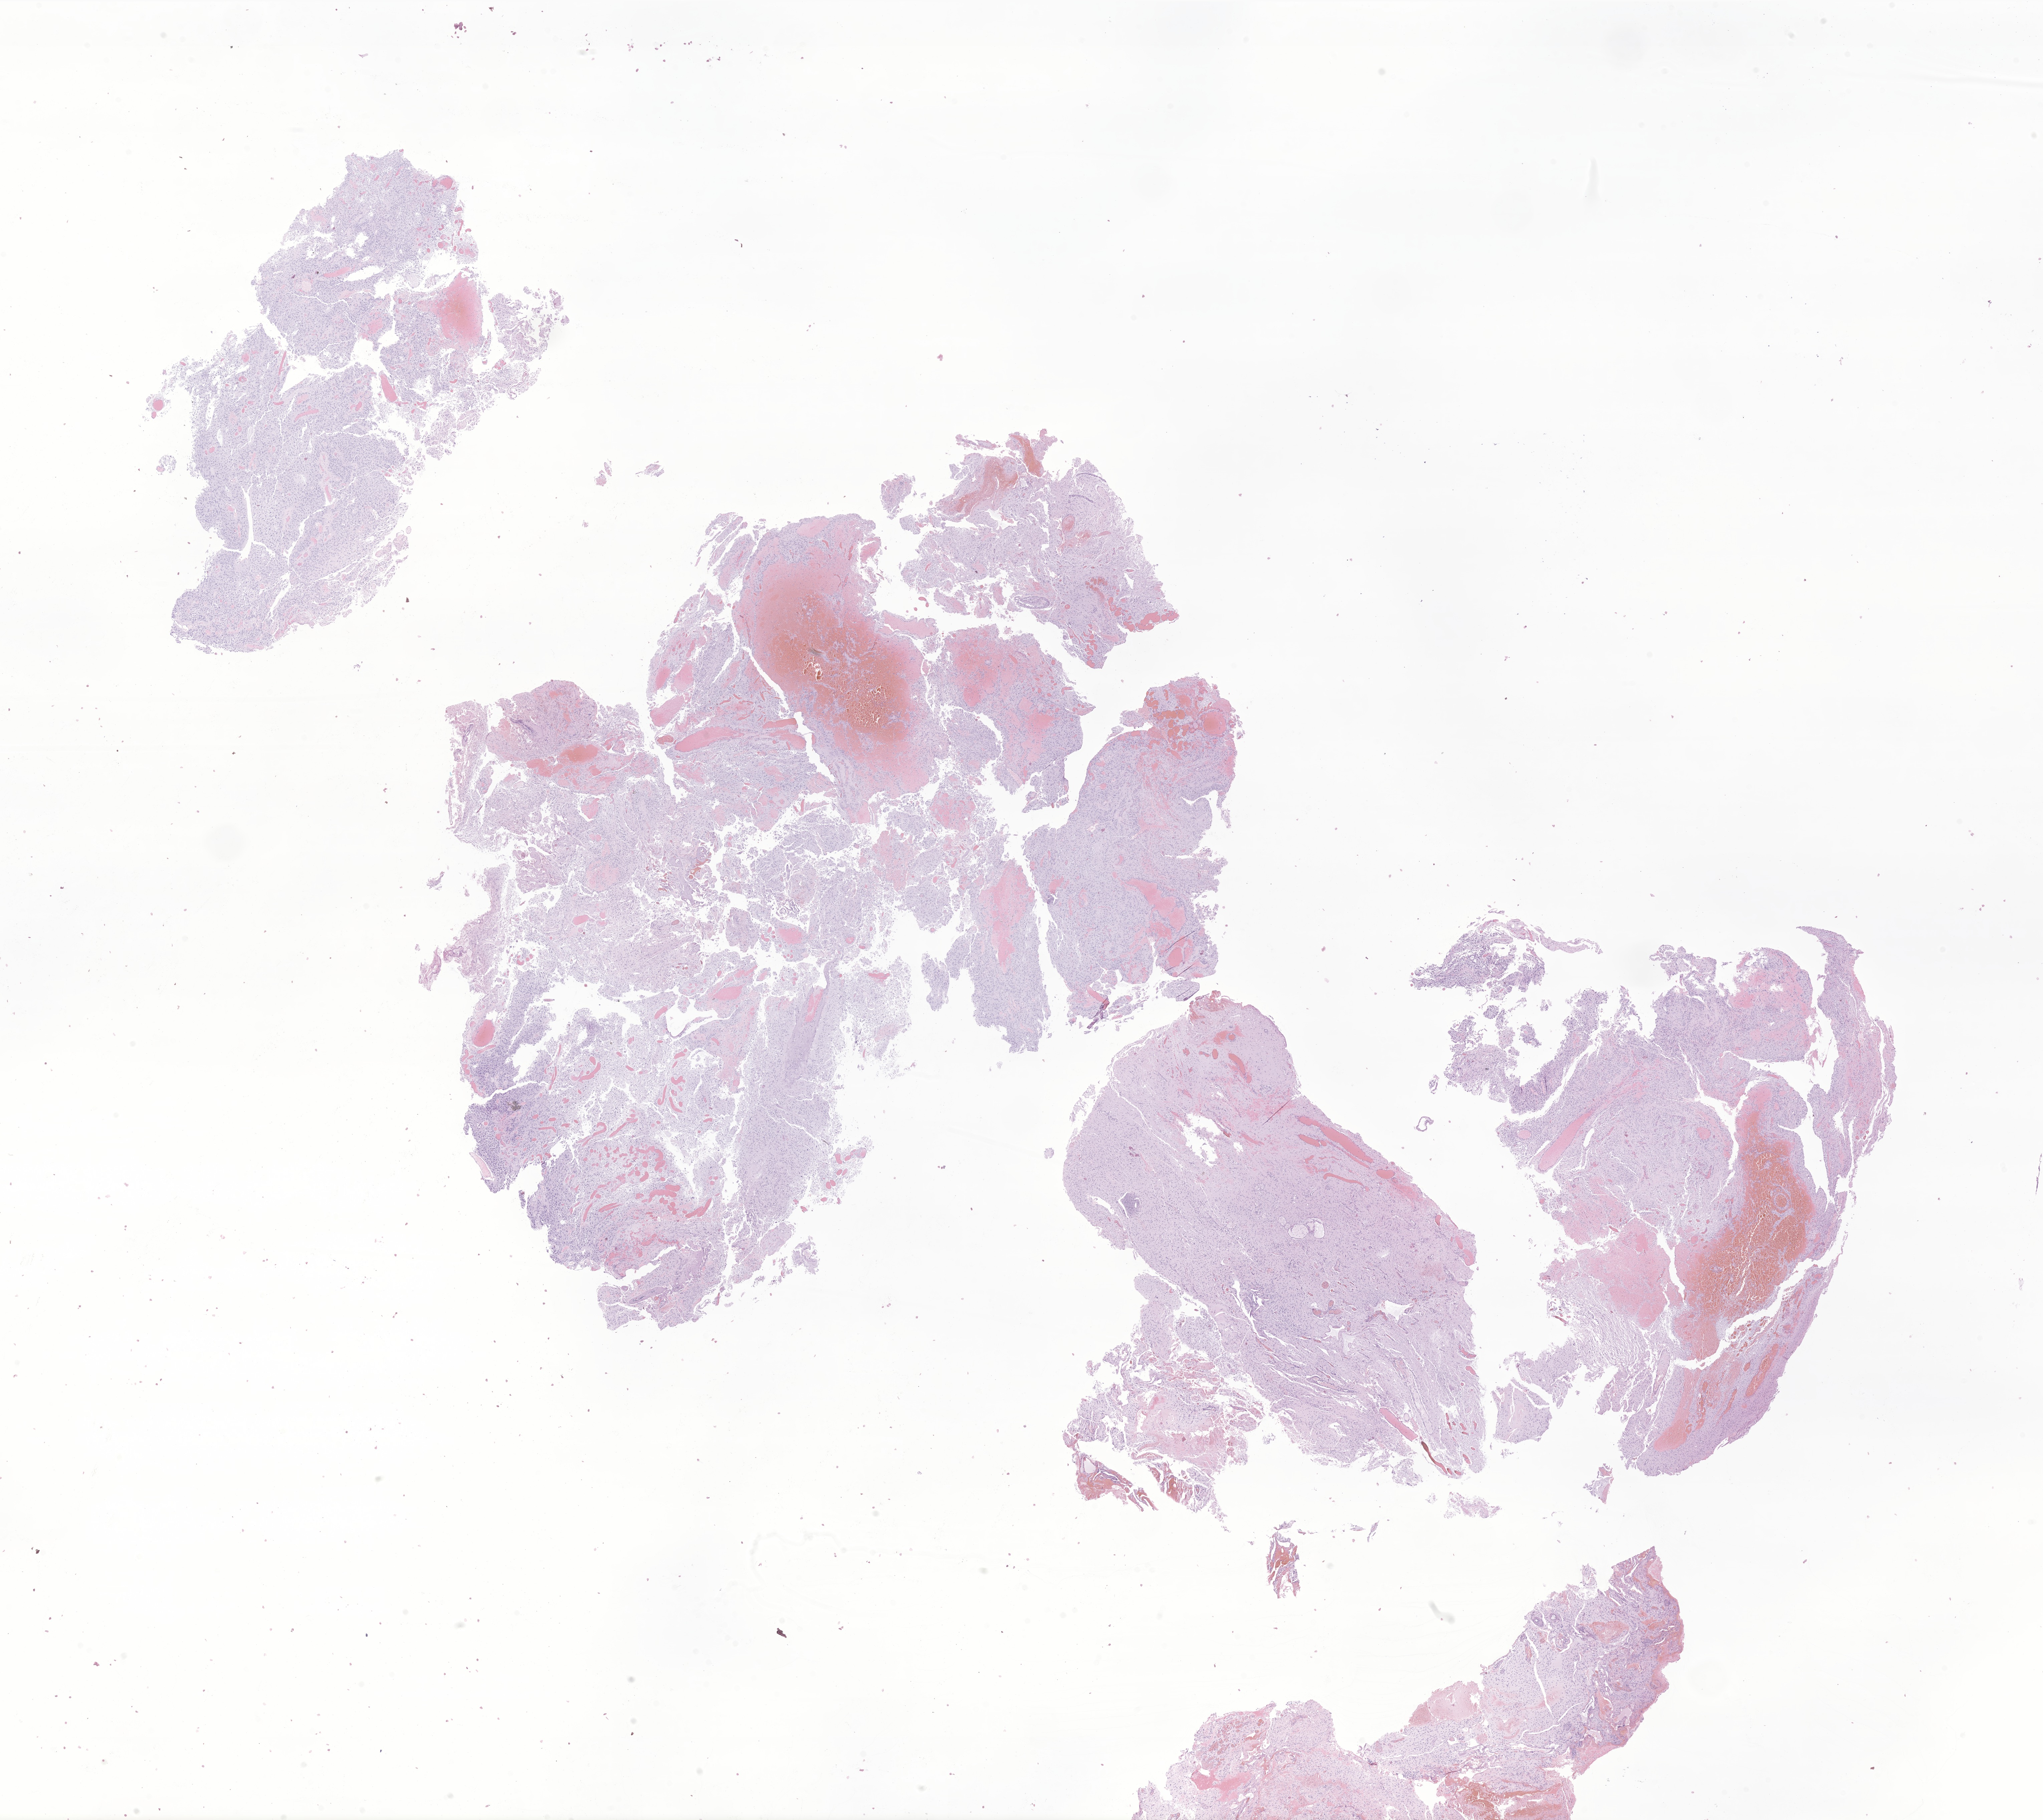
Haematoxylin and eosin whole-slide image of tumor tissue from the cerebellum — a low-resolution overview of the entire scanned area, about 25.8 x 23.0 mm; formalin-fixed paraffin-embedded section. Female patient, age 130 months (10 years 10 months).
- diagnosis (ICD-O-3 morphology term): Pilocytic astrocytoma